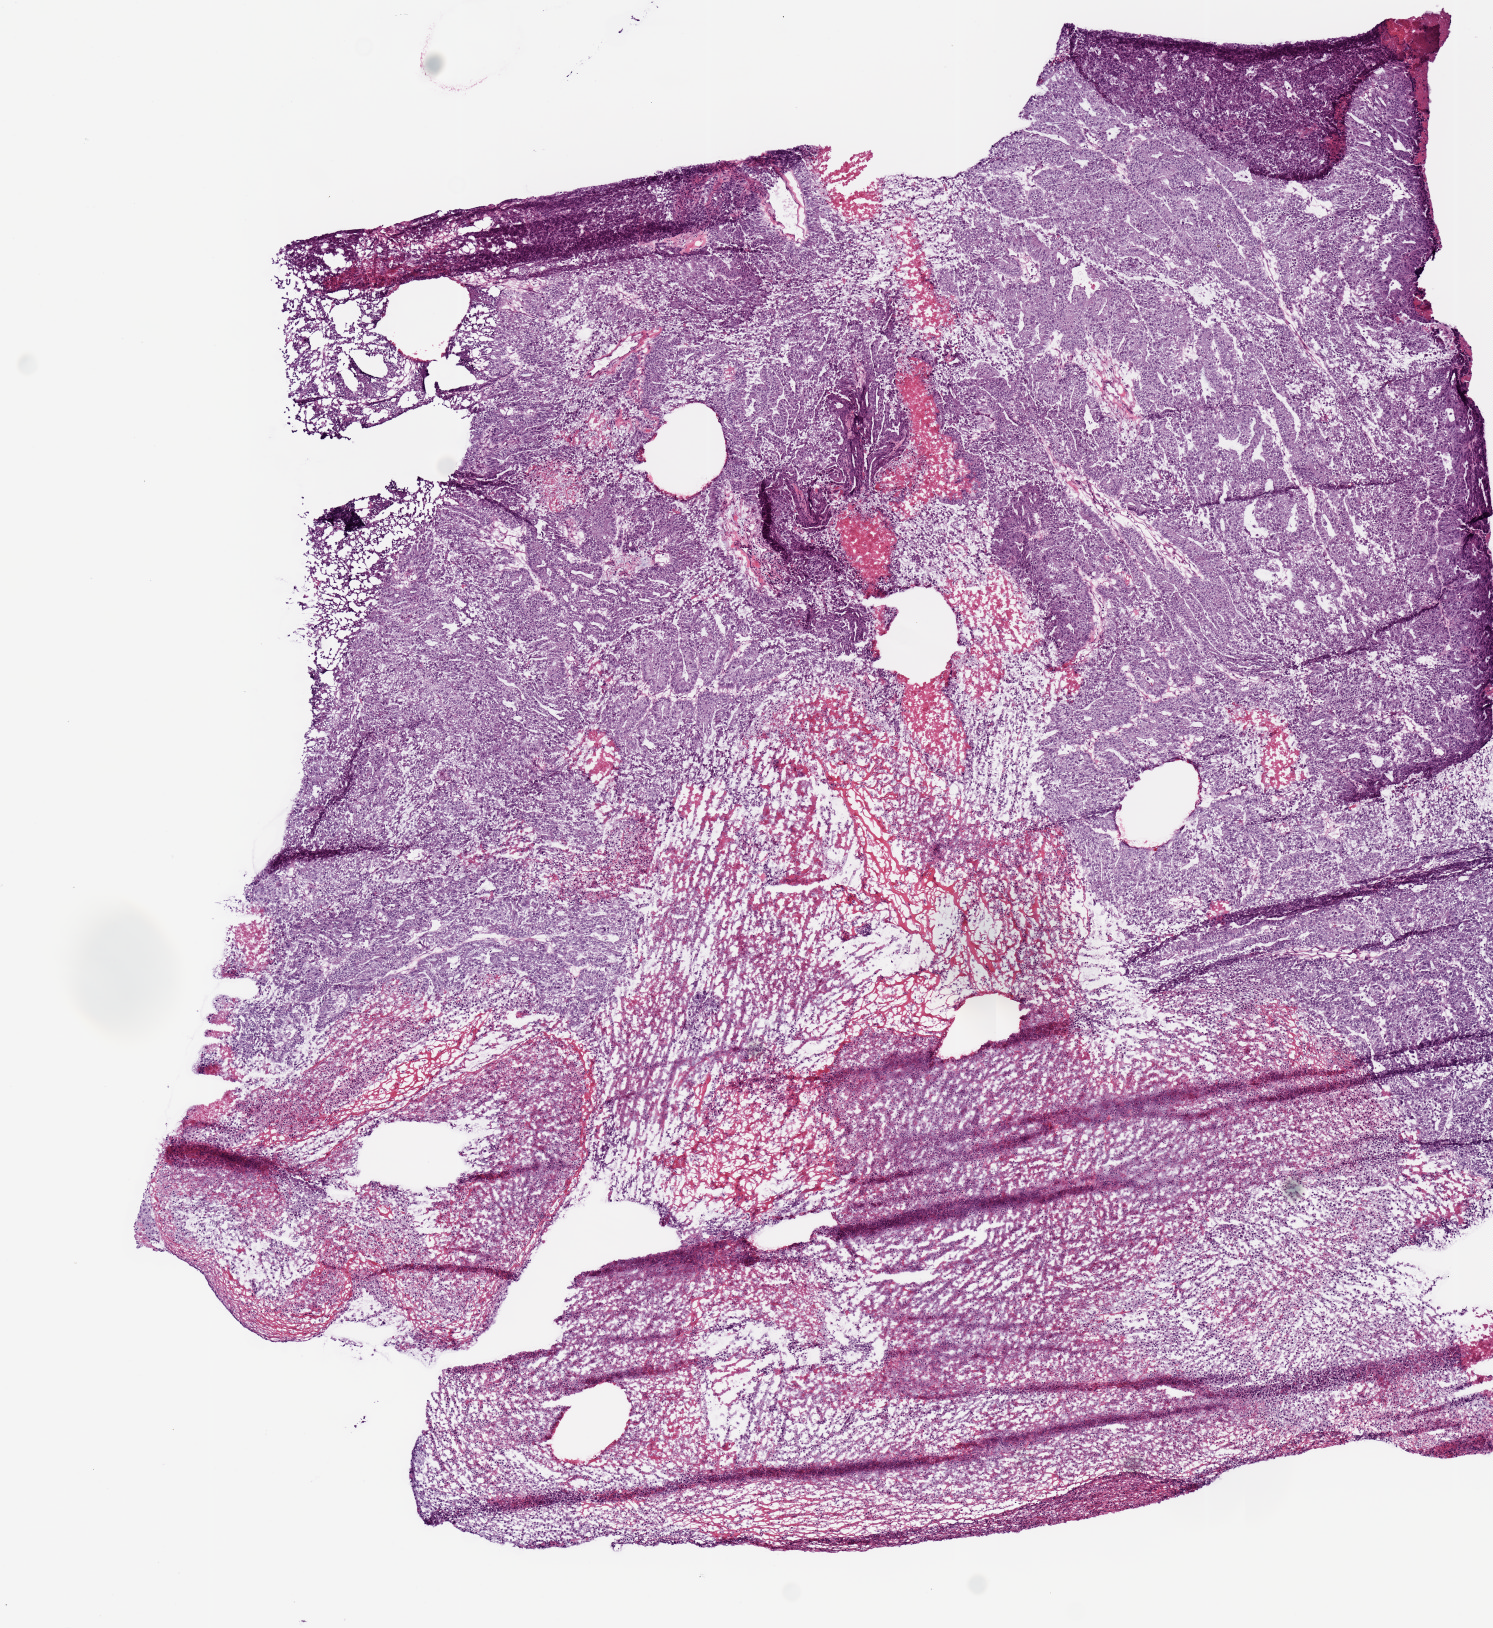
Whole-slide histology image, H&E-stained, low-resolution overview of the scanned area, about 5.9 x 6.4 mm (from a 20x scan), frozen section from the top of the tissue portion, sample: primary tumour, uterus. Female patient; age at initial diagnosis 65 years. Histologic grade: G3 (poorly differentiated). Slide review estimates, as recorded: tumour cells 95%, tumour nuclei 80%, normal cells 0%, stromal cells 0%, necrosis 5%. Infiltration values recorded for this section: lymphocyte infiltration 0%, monocyte infiltration 0%, neutrophil infiltration 0%.
FIGO stage: IA. Diagnosis: Endometrioid adenocarcinoma, NOS.